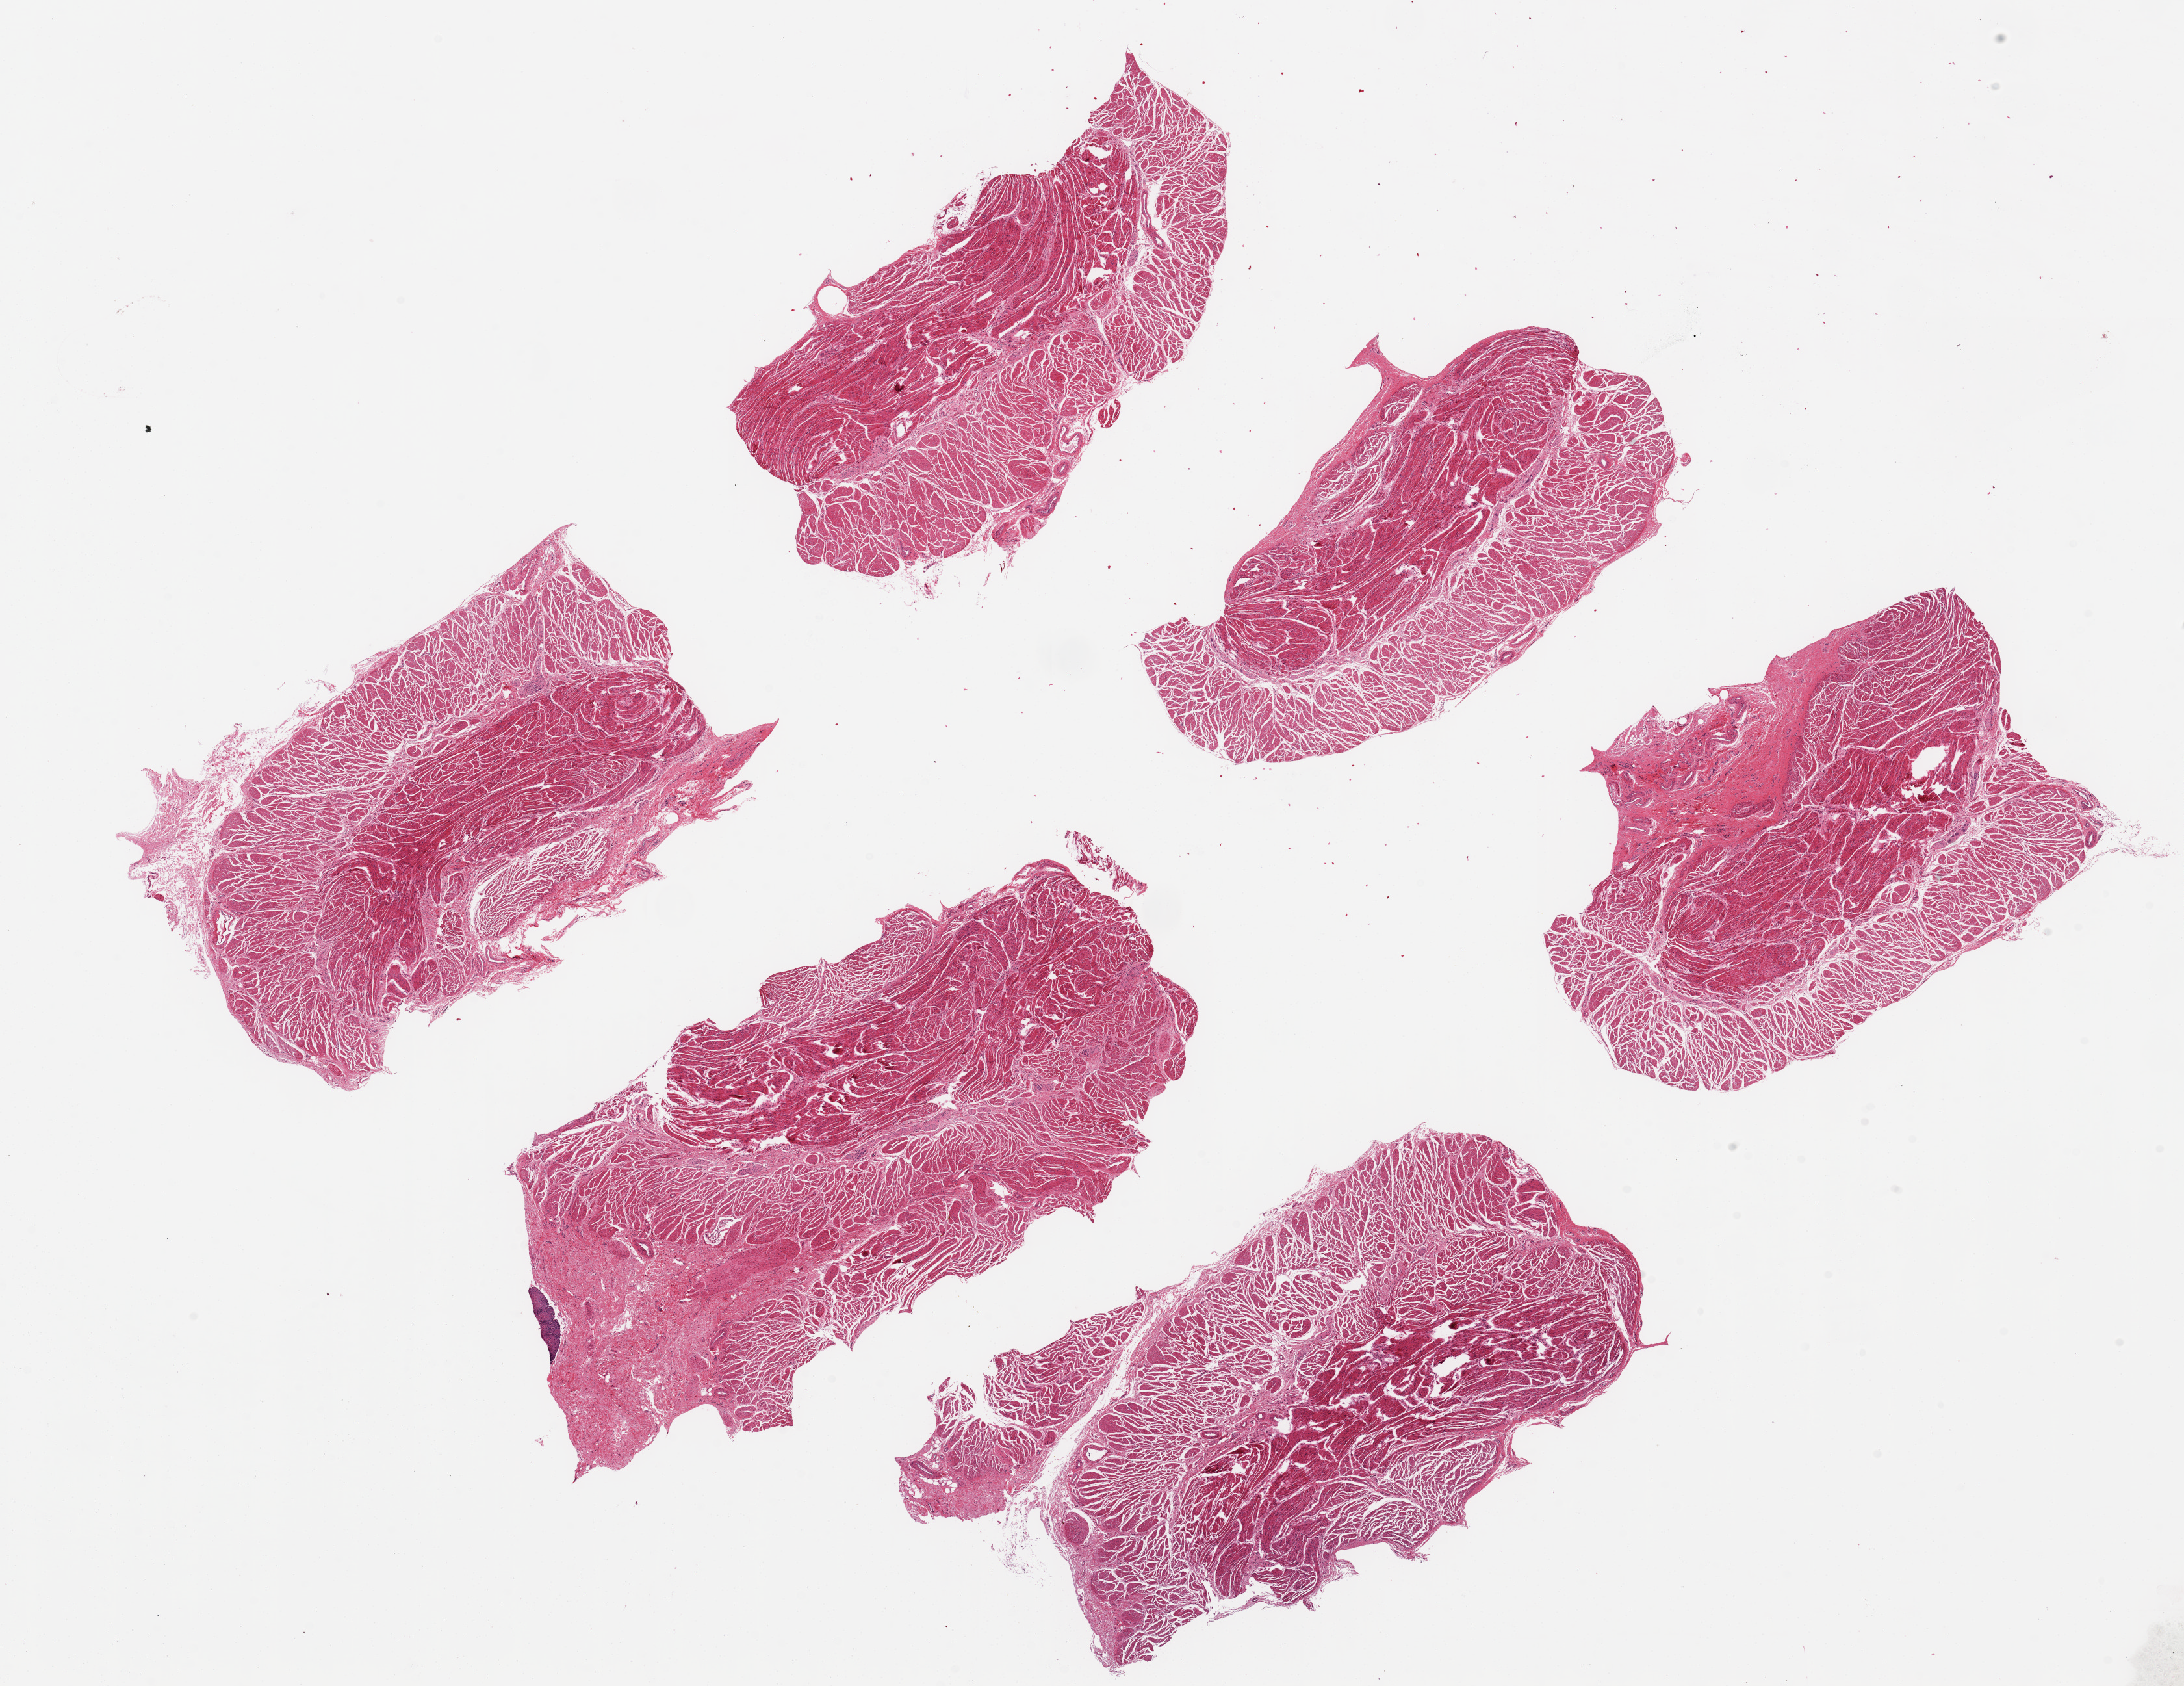
Haematoxylin and eosin whole-slide image, brightfield, shown as a low-resolution overview of the whole scanned area (about 26.6 x 20.5 mm, from a 20x scan); PAXgene-fixed, paraffin-embedded tissue; sampled site (target tissue): esophageal muscle; tissue donor sample. Donor sex: male.
* reviewer comment on this tissue sample: 6 ~7x4mm pieces